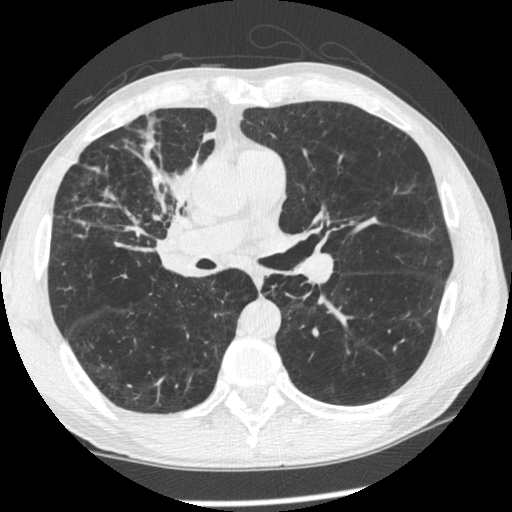
Low-dose screening chest CT, one axial slice. Position 131 of 261 along the scan axis. 120 kVp. Lung window (W 1500 / L -600 HU). 1.25 mm slice thickness. 512 × 512 image matrix.
Structures marked on this image (manually delineated by an expert):
- lesion 1 (tumor, upper lobe of right lung): bounding box (x1, y1, x2, y2) in pixels: (94, 121, 215, 236)